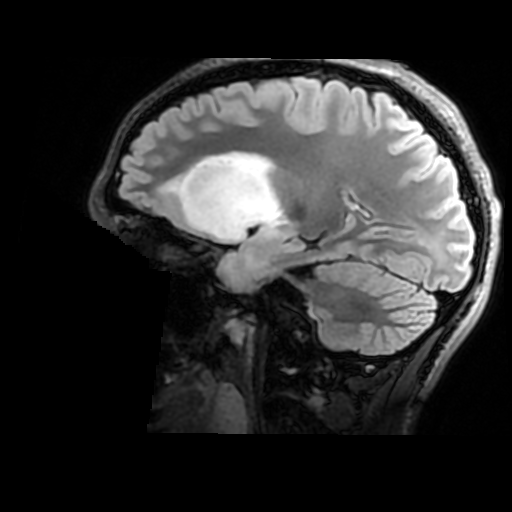
Brain MRI from a brain-tumour surgery series, one sagittal slice; position 108 of 176 along the scan axis; T2 FLAIR; 1 mm slice thickness; 512 × 512 image matrix, field of view 240 × 240 mm. From the clinical record (not read from this slice): histopathology: Astrocytoma; WHO grade: 2; IDH mutation: yes; tumour location: Right Insular.
Annotated regions visible in this slice (manually delineated by an expert):
- tumour: bounding box <171,152,284,274> (left, top, right, bottom; pixels)